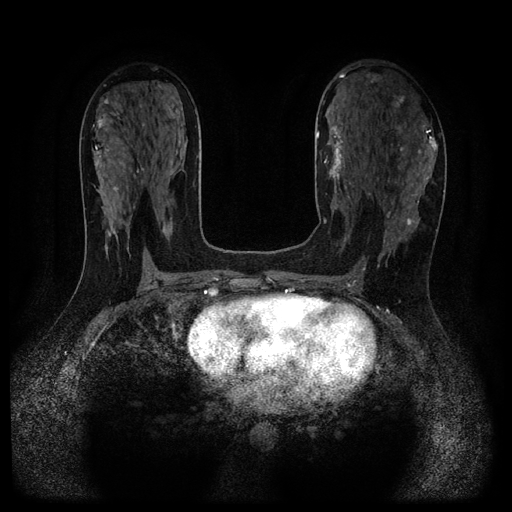
Breast MRI (dynamic contrast-enhanced, multi-phase), one axial slice; slice 58 of 116 in the series (ordered by position); dynamic contrast-enhanced series, time point 2 of 5 at this slice position (early post-contrast); 1.5 T; TE 2.7 ms, TR 5.4 ms; 2.2 mm slice thickness; 512 × 512 image matrix, field of view 330 × 330 mm. Female patient, age 43 years.
Structures marked on this image (semi-automatically segmented with operator editing):
- breast lesion (labelled benign in the annotation): bounding box [x1, y1, x2, y2] px = [321, 117, 347, 202]